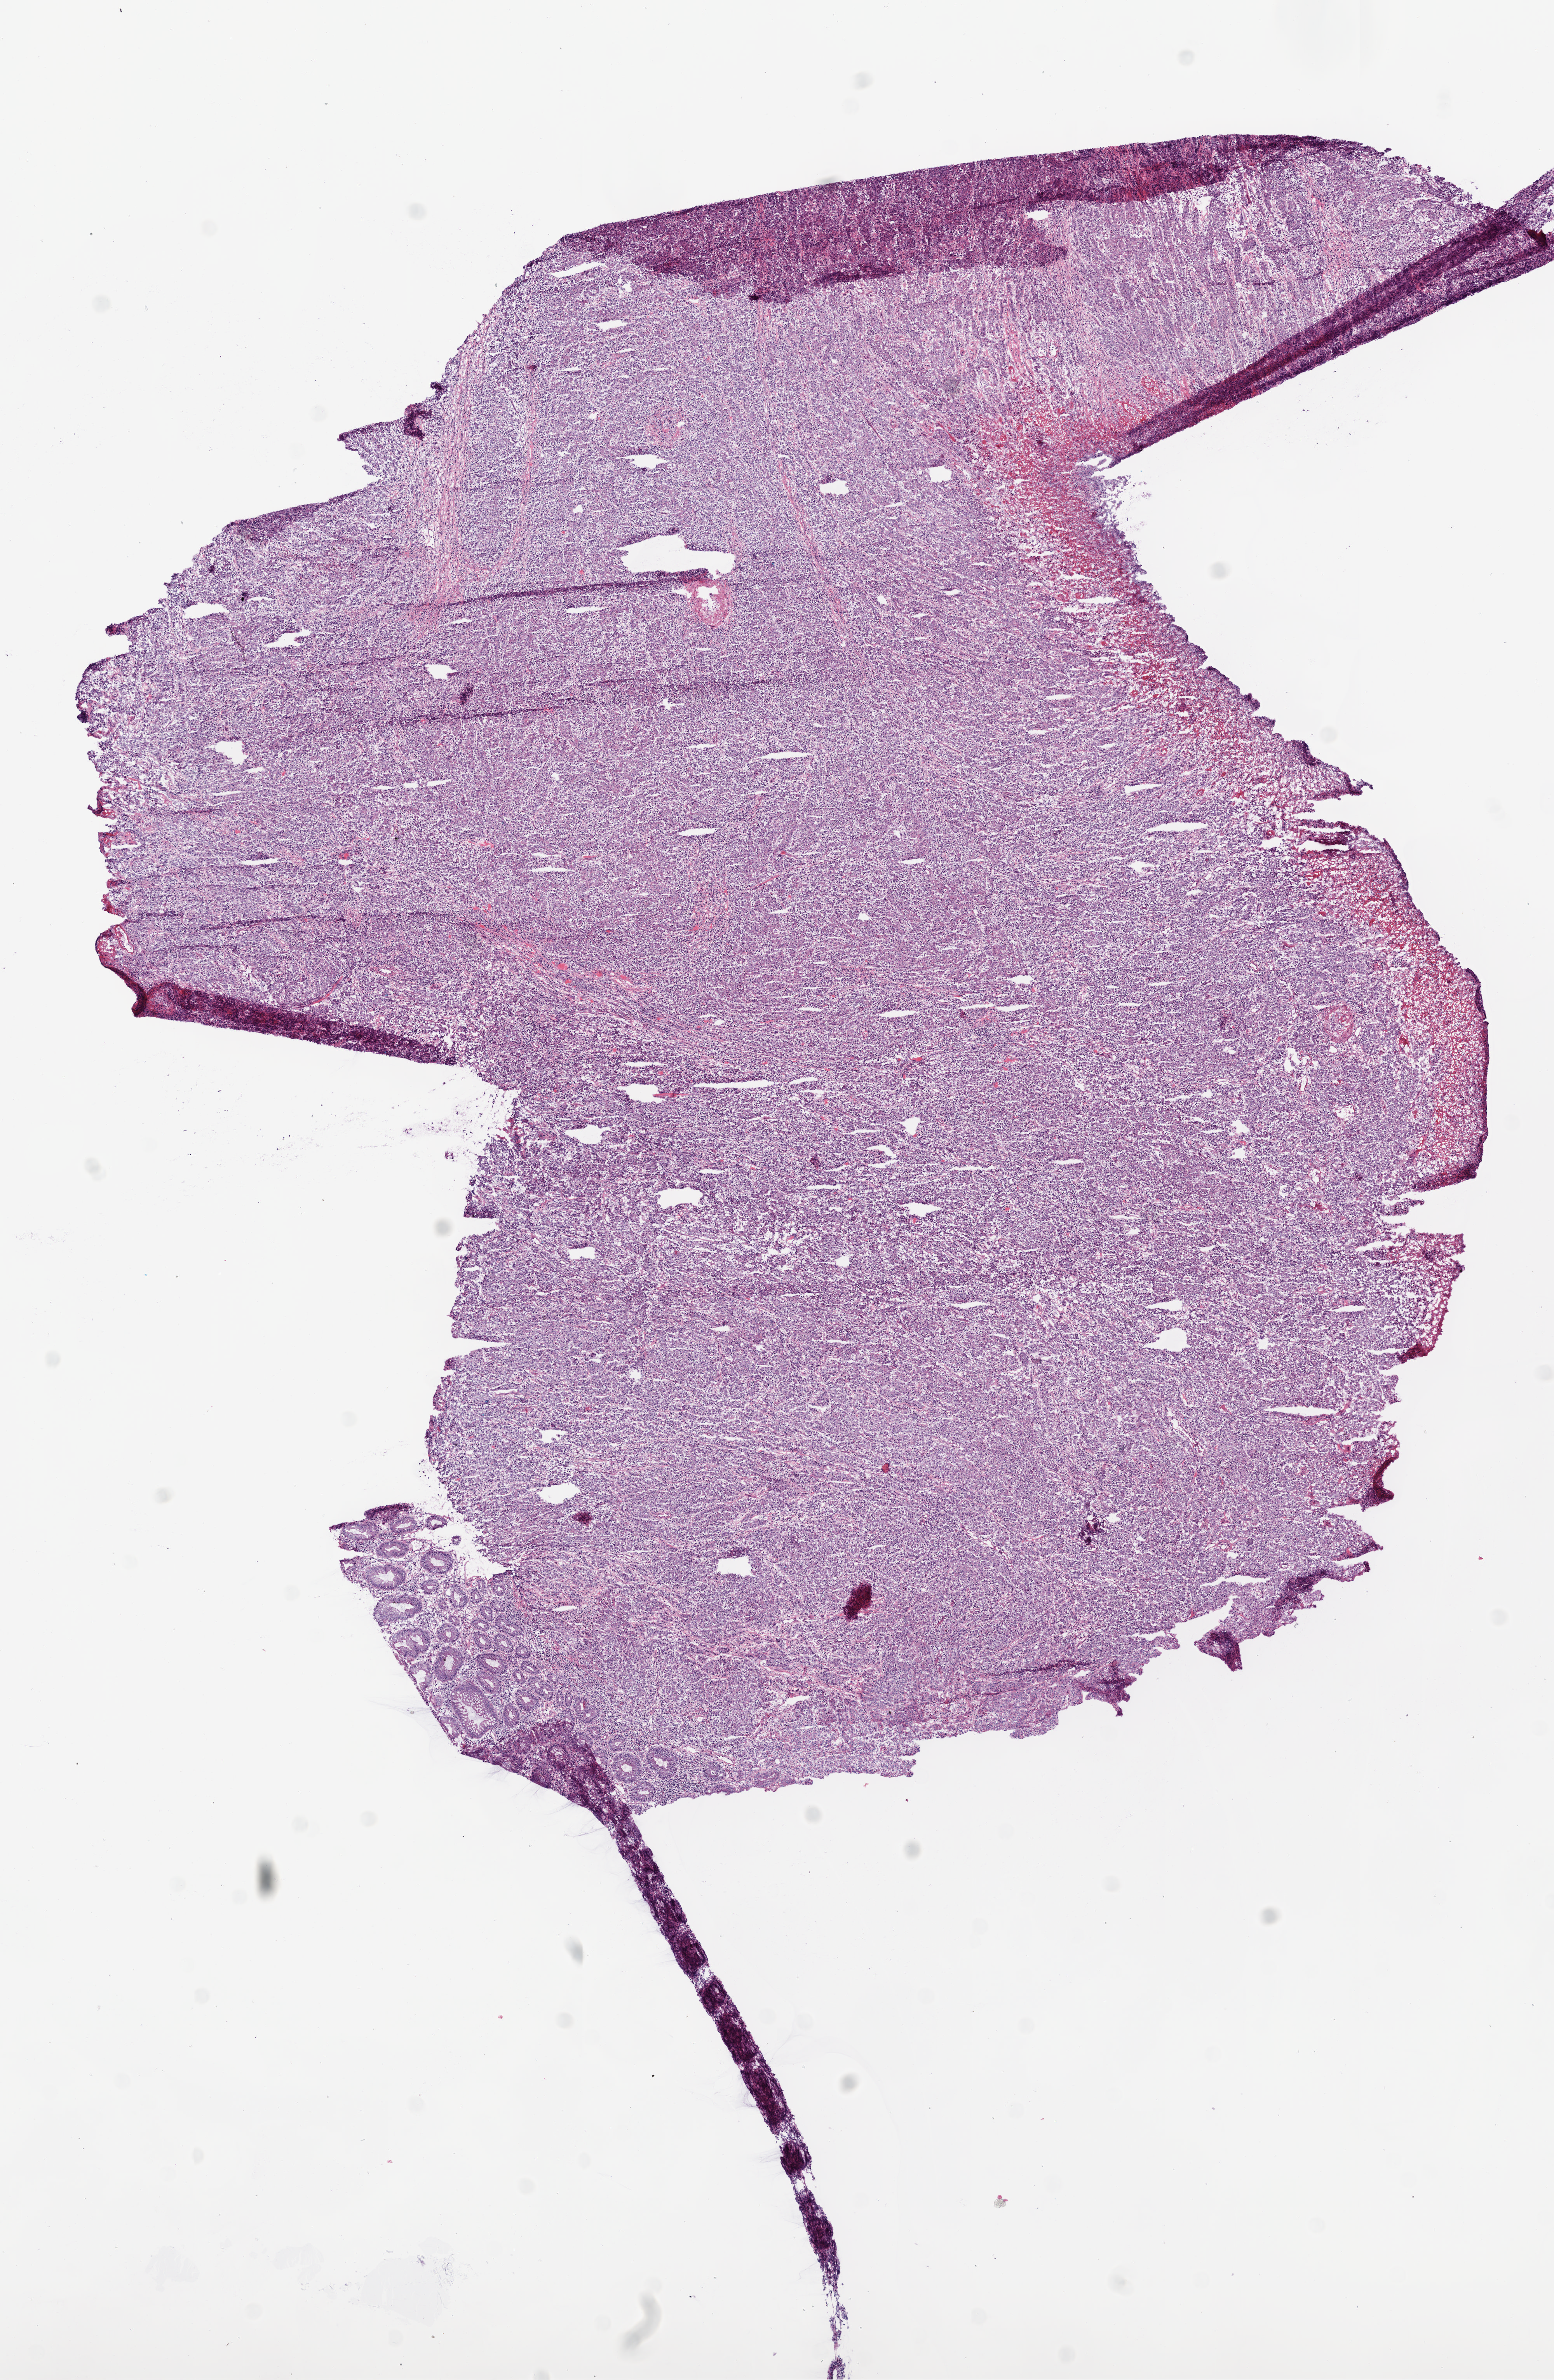
Whole-slide histology image, H&E, shown as a low-resolution overview of the whole scanned area (about 8.0 x 12.3 mm); frozen section; primary tumour sample from the colon. Patient: female, age at initial diagnosis 80 years. Pathologist review of this section (percent, as recorded): tumour cells 95%, tumour nuclei 80%, normal cells 4%, necrosis 1%. Infiltration values recorded for this section: lymphocyte infiltration 1%, neutrophil infiltration 19%.
Lymph nodes positive (case pathology): 0 of 20 examined. AJCC pathologic stage: IIA (6th edition). Pathologic diagnosis: Adenocarcinoma, NOS (ascending colon).